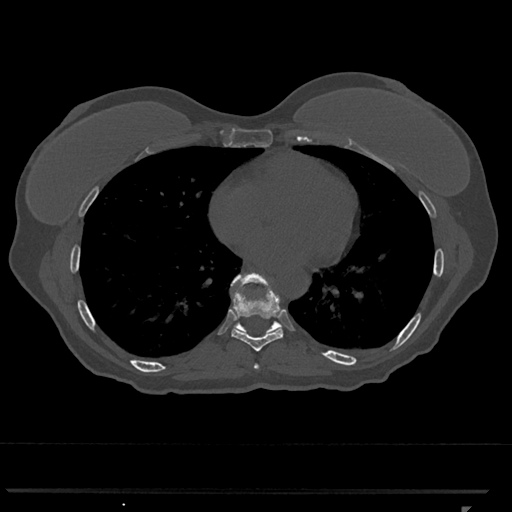
CT including the spine, one axial slice. Position 654 of 793 along the scan axis. Reconstruction kernel Br40s/3. Bone window (W 1800 / L 400 HU). 0.5 mm slice thickness. 512 × 512 image matrix. Female patient, age 62 years. From the clinical record (not read from this slice): primary cancer: renal.
Outlined on this slice (semi-automatically segmented with operator editing):
- T7 vertebra: box from (x=254, y=363) to (x=259, y=369) px
- T8 vertebra: (x=231, y=287)–(x=283, y=351)
- T9 vertebra: (x=231, y=272)–(x=282, y=335)